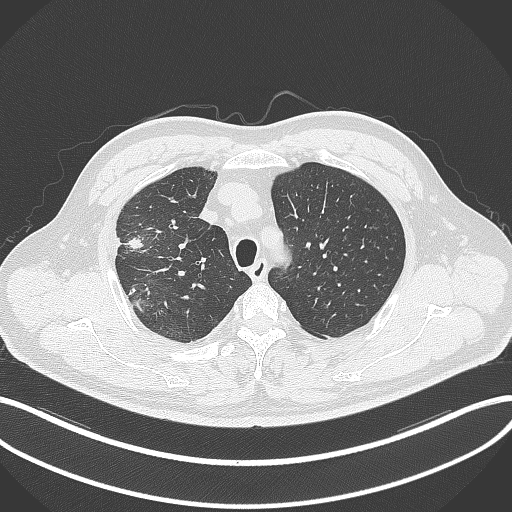
Chest CT, one axial slice; slice 272 of 348 in the series (ordered by position); reconstruction kernel B70f; lung window (W 1500 / L -600 HU); 512 × 512 image matrix, field of view 400 × 400 mm. Male patient, age 55 years. From the clinical record (not read from this slice): clinical TNM (as recorded): T3 N2 M1.
Annotated regions visible in this slice (rectangle marked by the reading radiologist):
- lung tumour (recorded histology: adenocarcinoma): bounding box <124,233,146,252> (left, top, right, bottom; pixels)